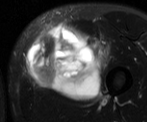
MRI of an extremity soft-tissue mass, one axial slice. Slice 23 of 52 in the series (ordered by position). T2-weighted fat-saturated. MR volume resampled by the dataset authors to the PET/CT grid (not the native acquisition matrix). 3.27 mm slice thickness. 147 × 122 image matrix, field of view 144 × 119 mm. Male patient. Case-level facts recorded for this patient, not image findings: histological type: pleiomorphic liposarcoma; grade: high; site of the primary tumour: left thigh.
Annotated regions visible in this slice (expert contour drawn on MRI and transferred to this co-registered scan by the dataset authors):
- gross tumour volume including surrounding oedema: bounding box (x1, y1, x2, y2) in pixels: (25, 21, 111, 102)
- gross tumour volume (mass): (27, 21, 104, 100)